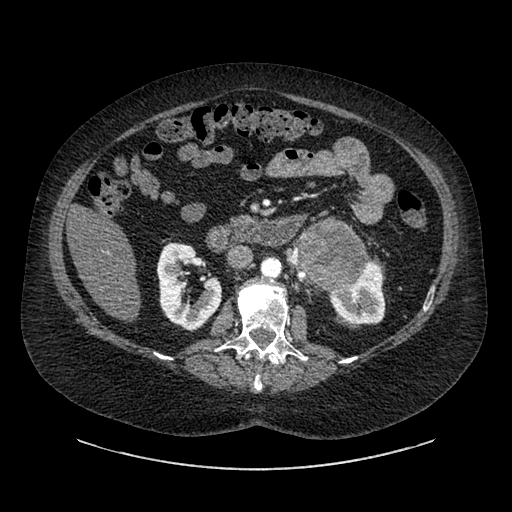
Contrast-enhanced abdominal CT, one axial slice; slice 510 of 769 in the series (ordered by position); 120 kVp; intravenous contrast given; soft-tissue window (W 400 / L 40 HU); 0.62 mm slice thickness; 512 × 512 image matrix, field of view 460 × 460 mm. Female patient, age 61 years. Case-level facts recorded for this patient, not image findings: diagnosis: adrenocortical carcinoma; tumour side: left adrenal; tumour size at pathology: 13 cm; Ki-67 index: 79 %.
Structures marked on this image (semi-automatic segmentation, software-assisted and operator-edited):
- mass: bounding box [x1, y1, x2, y2] px = [300, 223, 363, 286]